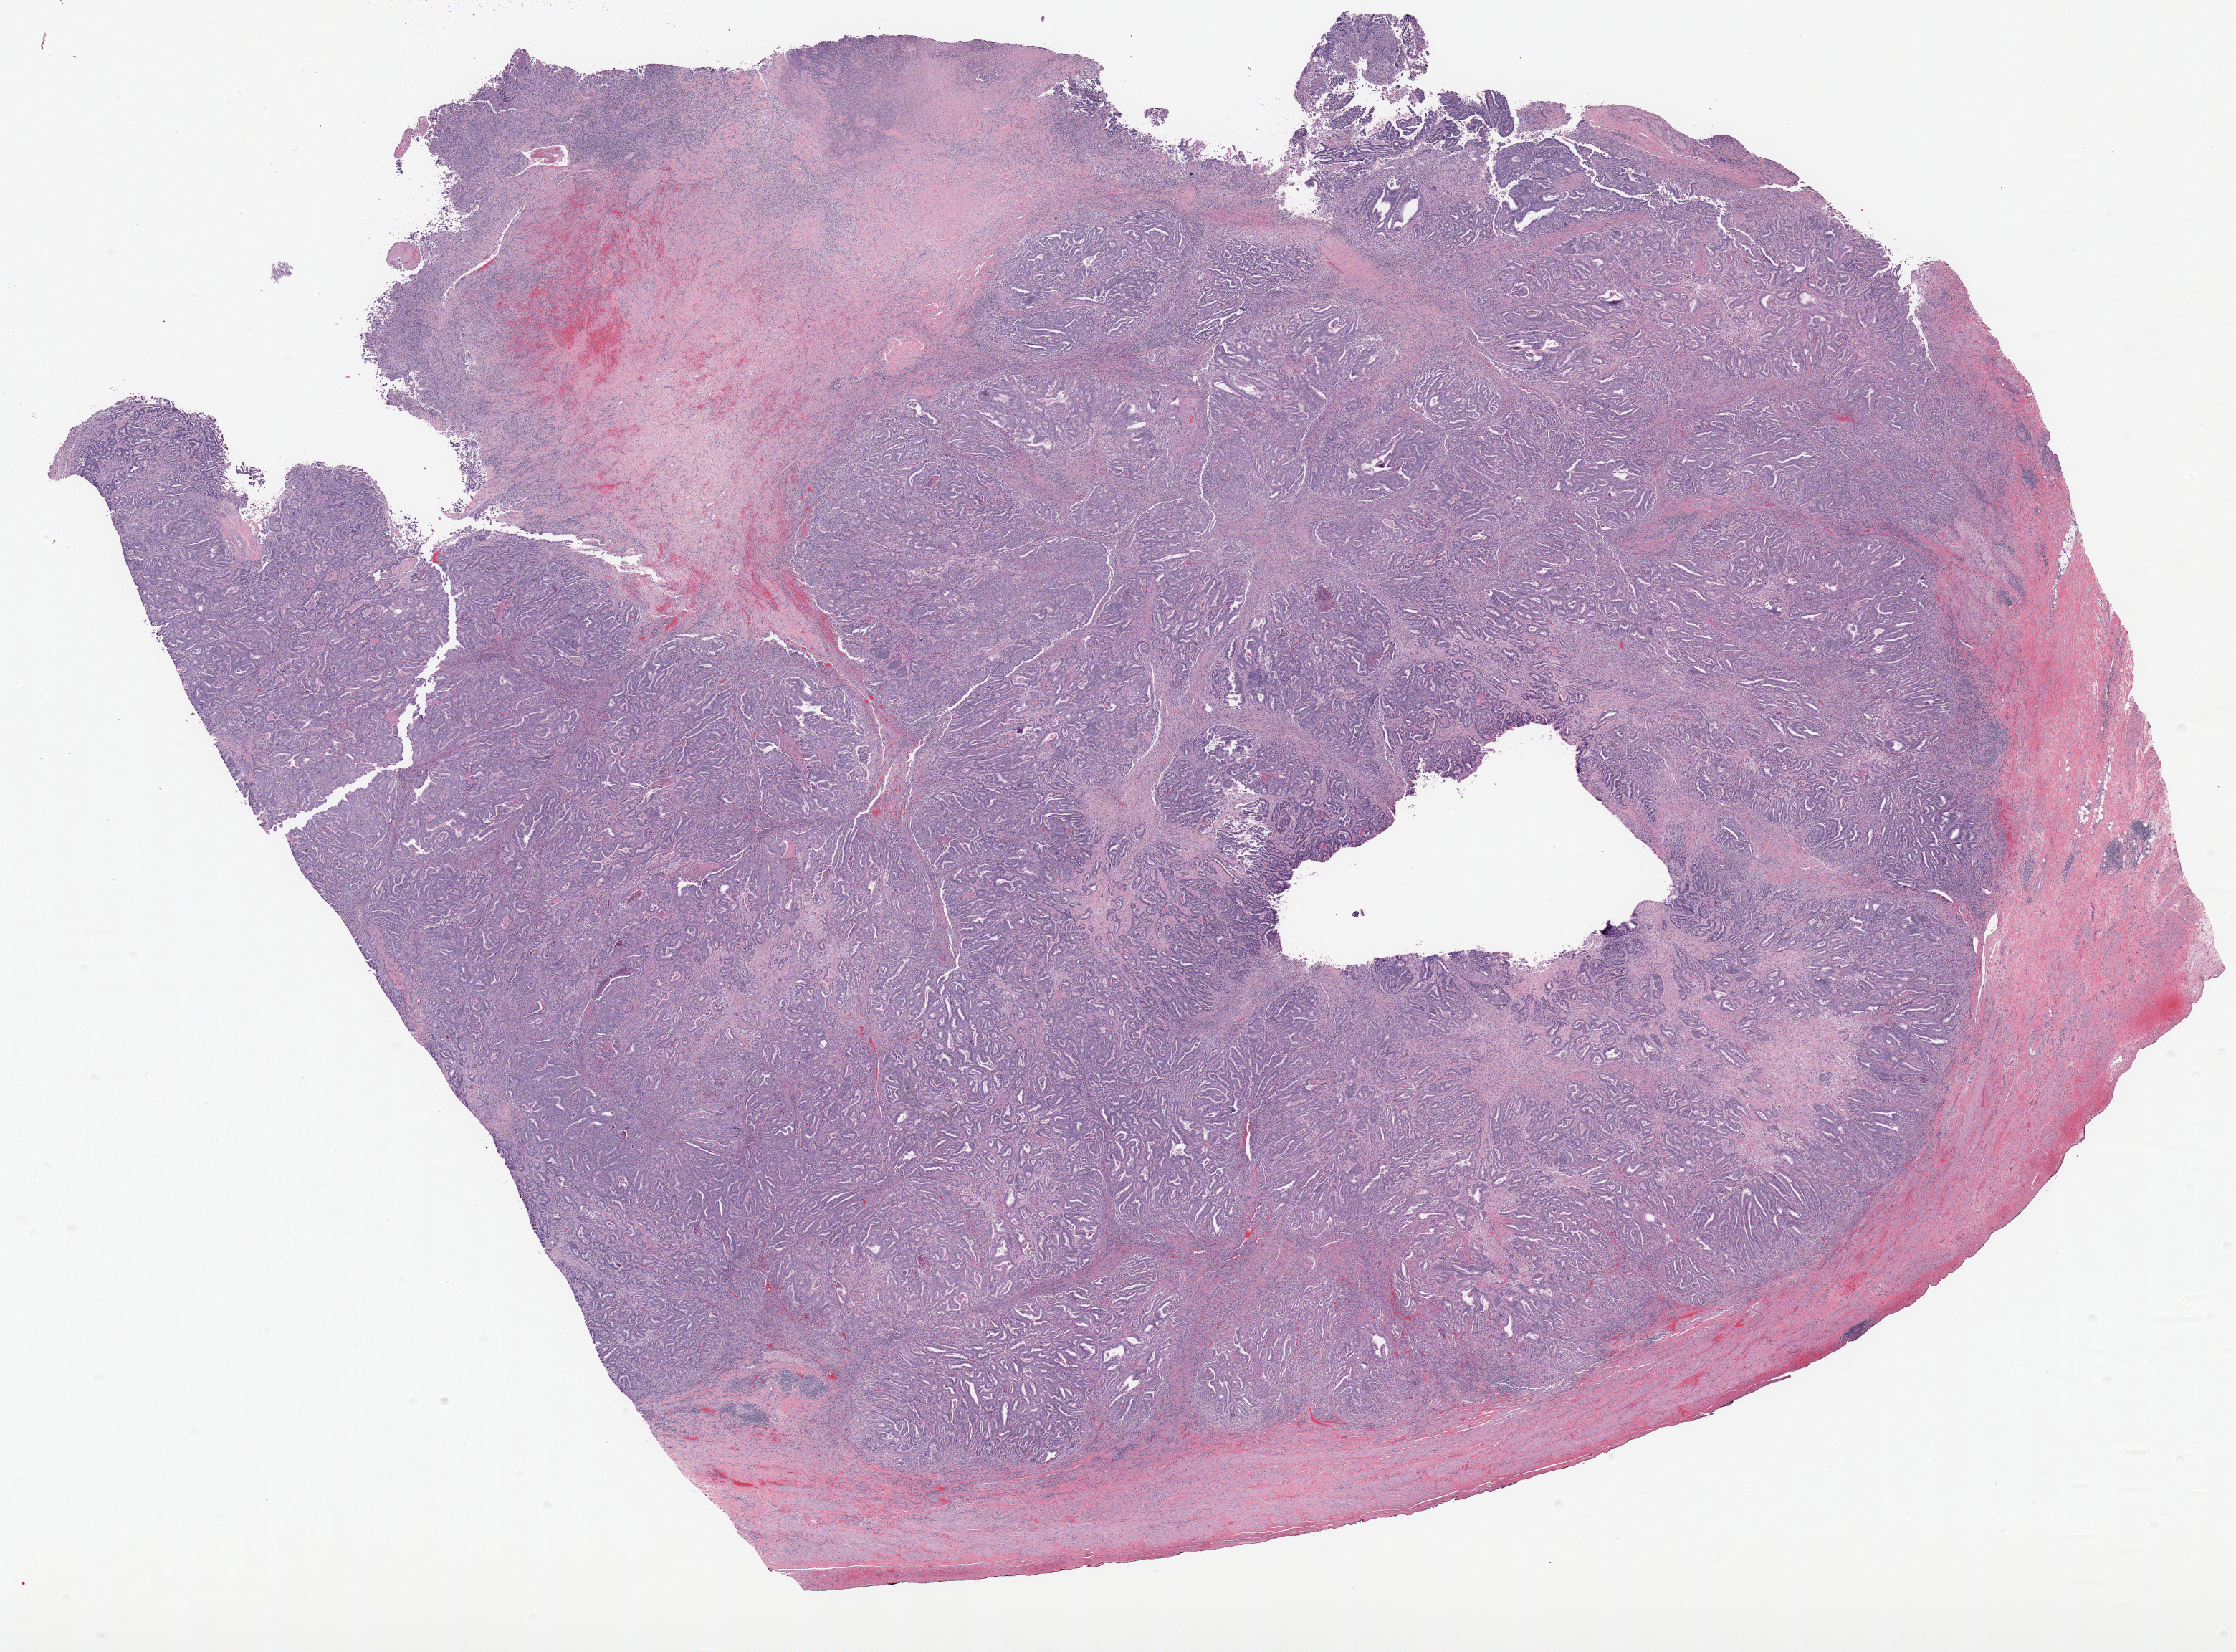
H&E whole-slide image, shown as a low-resolution overview of the whole scanned area (about 24.9 x 18.4 mm); FFPE section; sample: primary tumour, uterus. Female patient; age at initial diagnosis 59 years. Histologic grade: G3 (poorly differentiated).
• FIGO stage: II
• diagnosis: Endometrioid adenocarcinoma, NOS (endometrium)